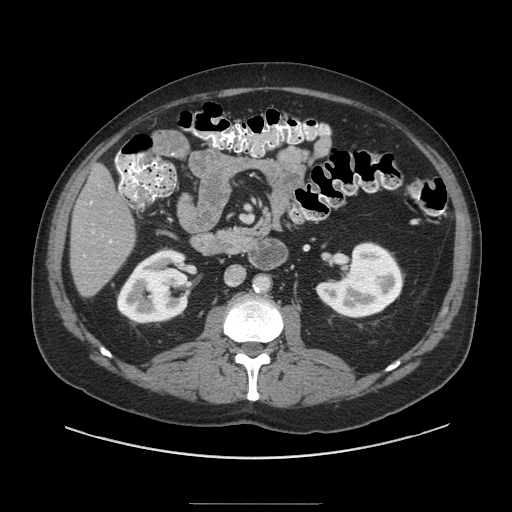
Contrast-enhanced abdominal CT (liver protocol), one axial slice; slice 31 of 91 in the series (ordered by position); soft-tissue window (W 400 / L 40 HU); 512 × 512 image matrix, field of view 440 × 440 mm. Case-level facts recorded for this patient, not image findings: diagnosis: hepatocellular carcinoma (patient treated with transarterial chemoembolisation; whether this scan precedes or follows treatment is not stated here); TNM stage (as recorded): Stage-I; Child-Pugh class: A; tumour differentiation: well differentiated; tumour size: 4 cm.
Structures marked on this image (semi-automatic segmentation, software-assisted and operator-edited):
- liver parenchyma outside the tumour (the mass and vessels are separate outlines, so this box may not span the whole liver): box from (x=70, y=164) to (x=136, y=296) px
- liver vessels: (x=90, y=202)–(x=112, y=243)